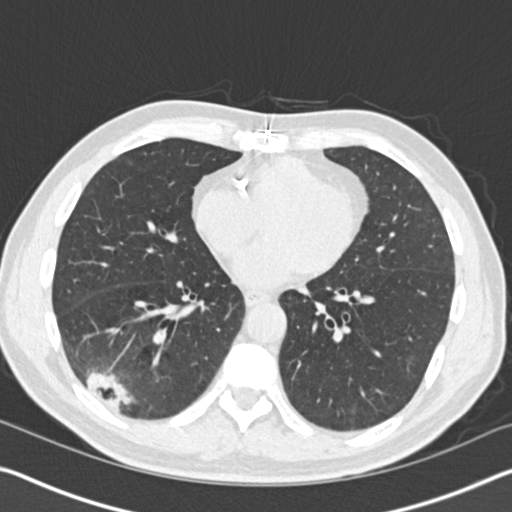
Axial slice from a low-dose chest CT screening exam, baseline screening round, lung window (W 1500 / L -600 HU), standard (soft-tissue) reconstruction kernel (B30f), 120 kVp, slice 95 of 161 in the series, 512 × 512 image matrix. Male participant, aged 61 years at enrolment. Current smoker at enrolment.
Expert reader's lesion annotation, box from (x=47, y=326) to (x=157, y=424) px. Reader record for this screening exam (exam-level; its link to the box is not recorded): non-calcified nodule or mass ≥4 mm, right lower lobe, 52 × 36 mm, spiculated (stellate) margins, soft tissue attenuation. Official screen result: positive, change unspecified: nodule(s) >= 4 mm or enlarging nodule(s), mass(es), or other non-specific abnormalities suspicious for lung cancer. Lung cancer was diagnosed 392 days after this screen (after the second annual screen): bronchiolo-alveolar adenocarcinoma, NOS, right lower lobe, moderately differentiated (G2), stage IIIB (AJCC 6th edition), 90 mm at pathology.